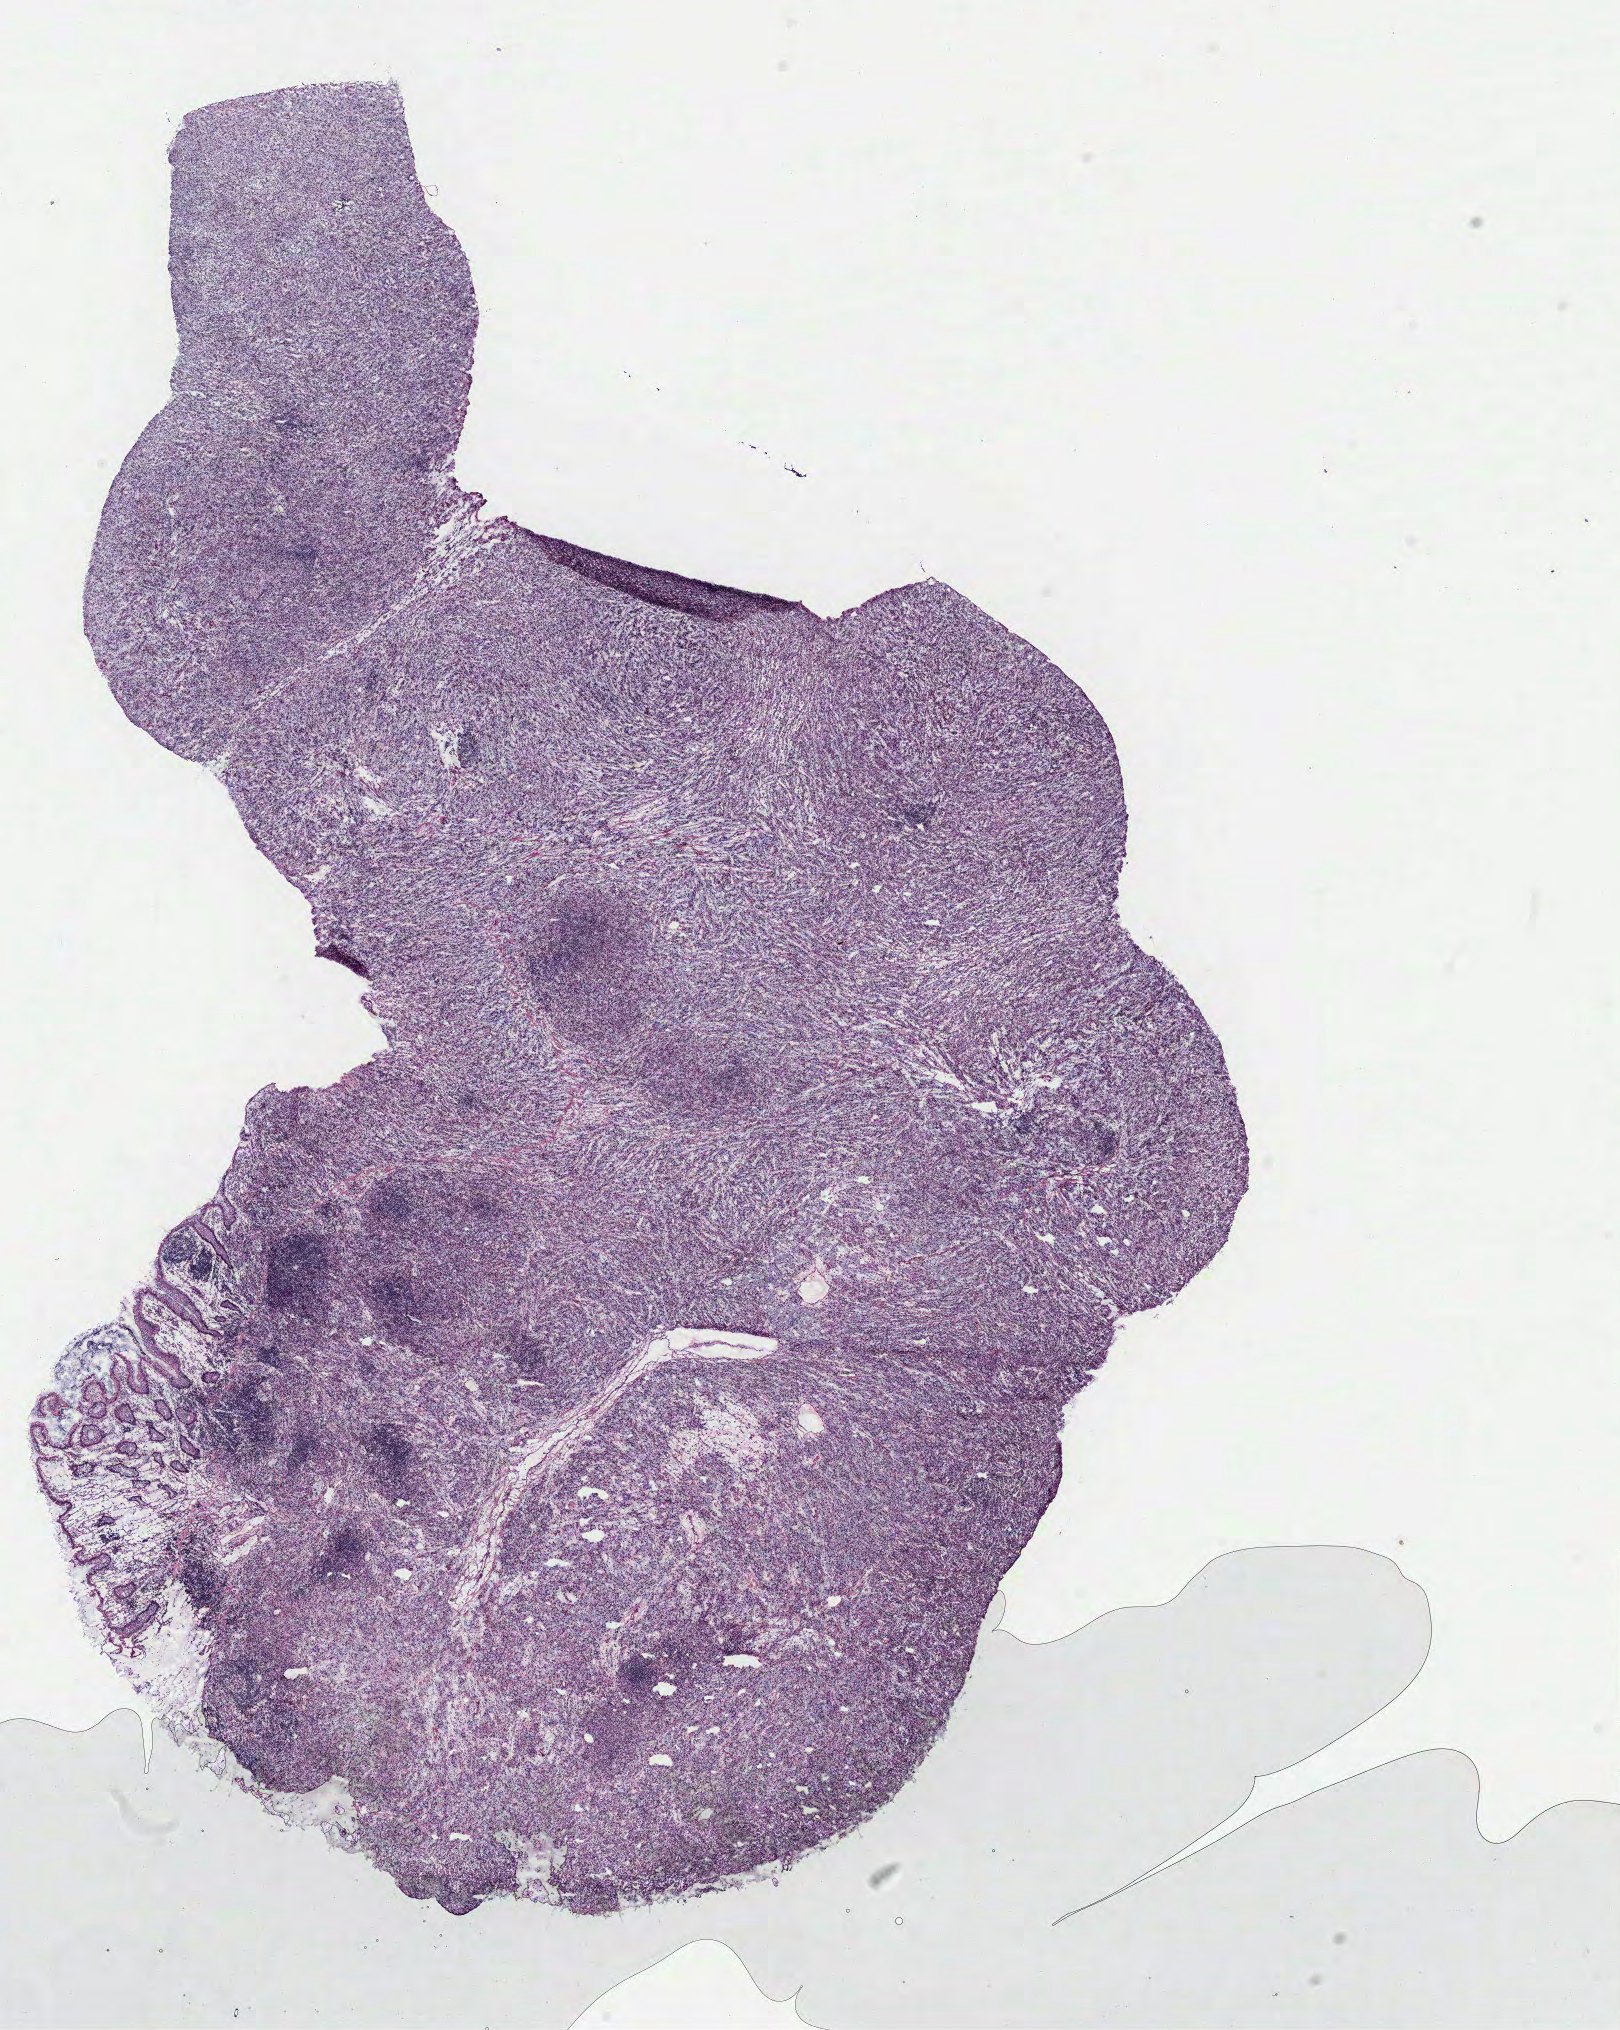
H&E whole-slide image, low-resolution overview of the scanned area, about 13.0 x 16.2 mm (acquisition: 40x scan), colon, normal (non-tumour) tissue. 75-year-old female patient.
This section: normal (non-tumour) tissue from the same patient. Patient diagnosis: Adenocarcinoma, NOS.